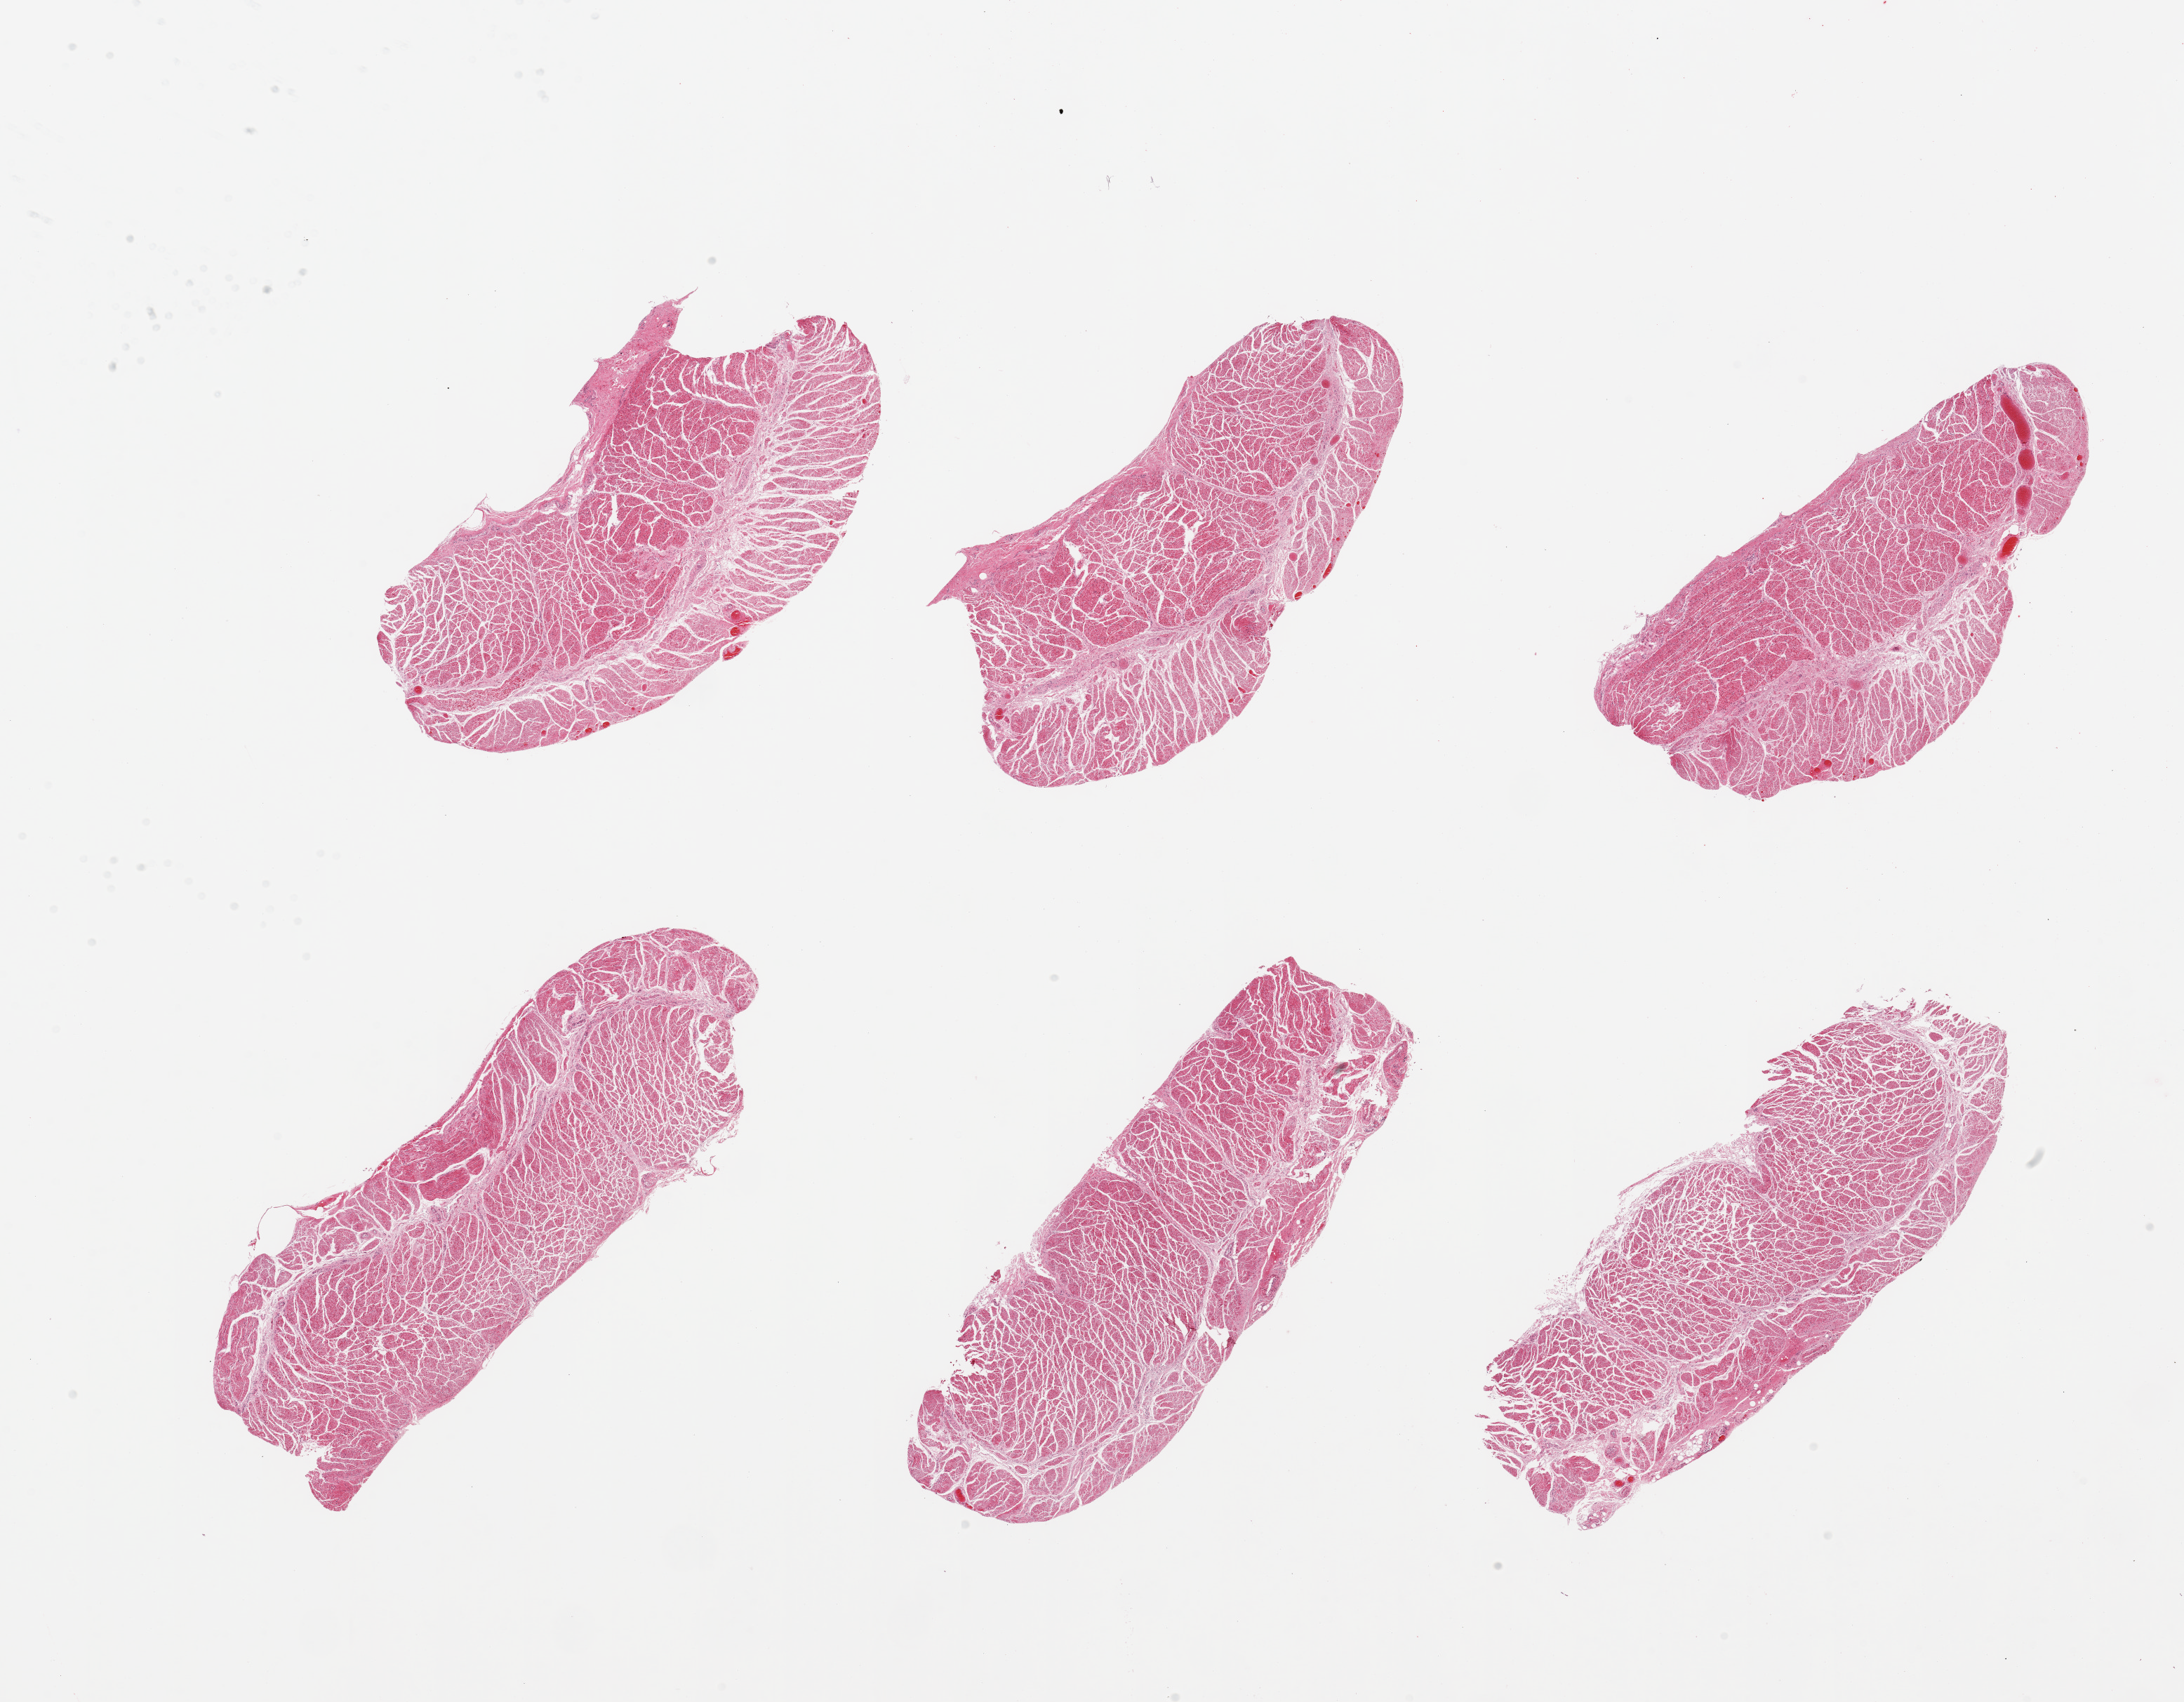
Whole-slide image, H&E stain, shown as a low-resolution overview of the whole scanned area (about 24.6 x 19.2 mm); PAXgene-fixed paraffin-embedded (PFPE) section; section of esophageal muscle (target tissue); donor tissue sample. Female donor.
* pathologist's review note for this sample: 6 pieces; well trimmed